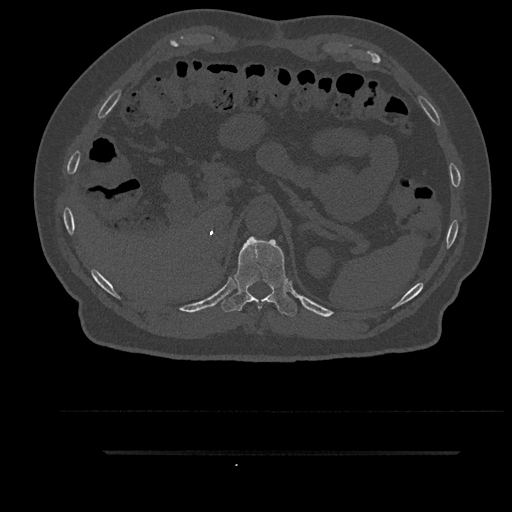
CT including the spine, one axial slice. Position 311 of 797 along the scan axis. 120 kVp. Bone window (W 1800 / L 400 HU). 0.5 mm slice thickness. 512 × 512 image matrix, field of view 432 × 432 mm. Patient: male, 63 years. Case-level facts recorded for this patient, not image findings: primary cancer: renal.
Outlined on this slice (semi-automatically segmented with operator editing):
- T11 vertebra: box from (x=221, y=236) to (x=298, y=316) px